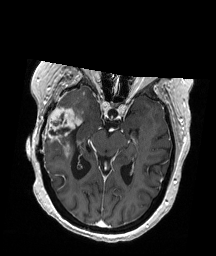
Brain MRI from a brain-tumour surgery series, one axial slice; slice 115 of 192 in the series (ordered by position); T1-weighted post-contrast; 1 mm slice thickness; 216 × 256 image matrix, field of view 211 × 250 mm. Case-level facts recorded for this patient, not image findings: histopathology: Glioblastoma; WHO grade: 4; IDH mutation: no.
Structures marked on this image (manually delineated by an expert):
- tumour: bounding box (x1, y1, x2, y2) in pixels: (42, 95, 82, 157)